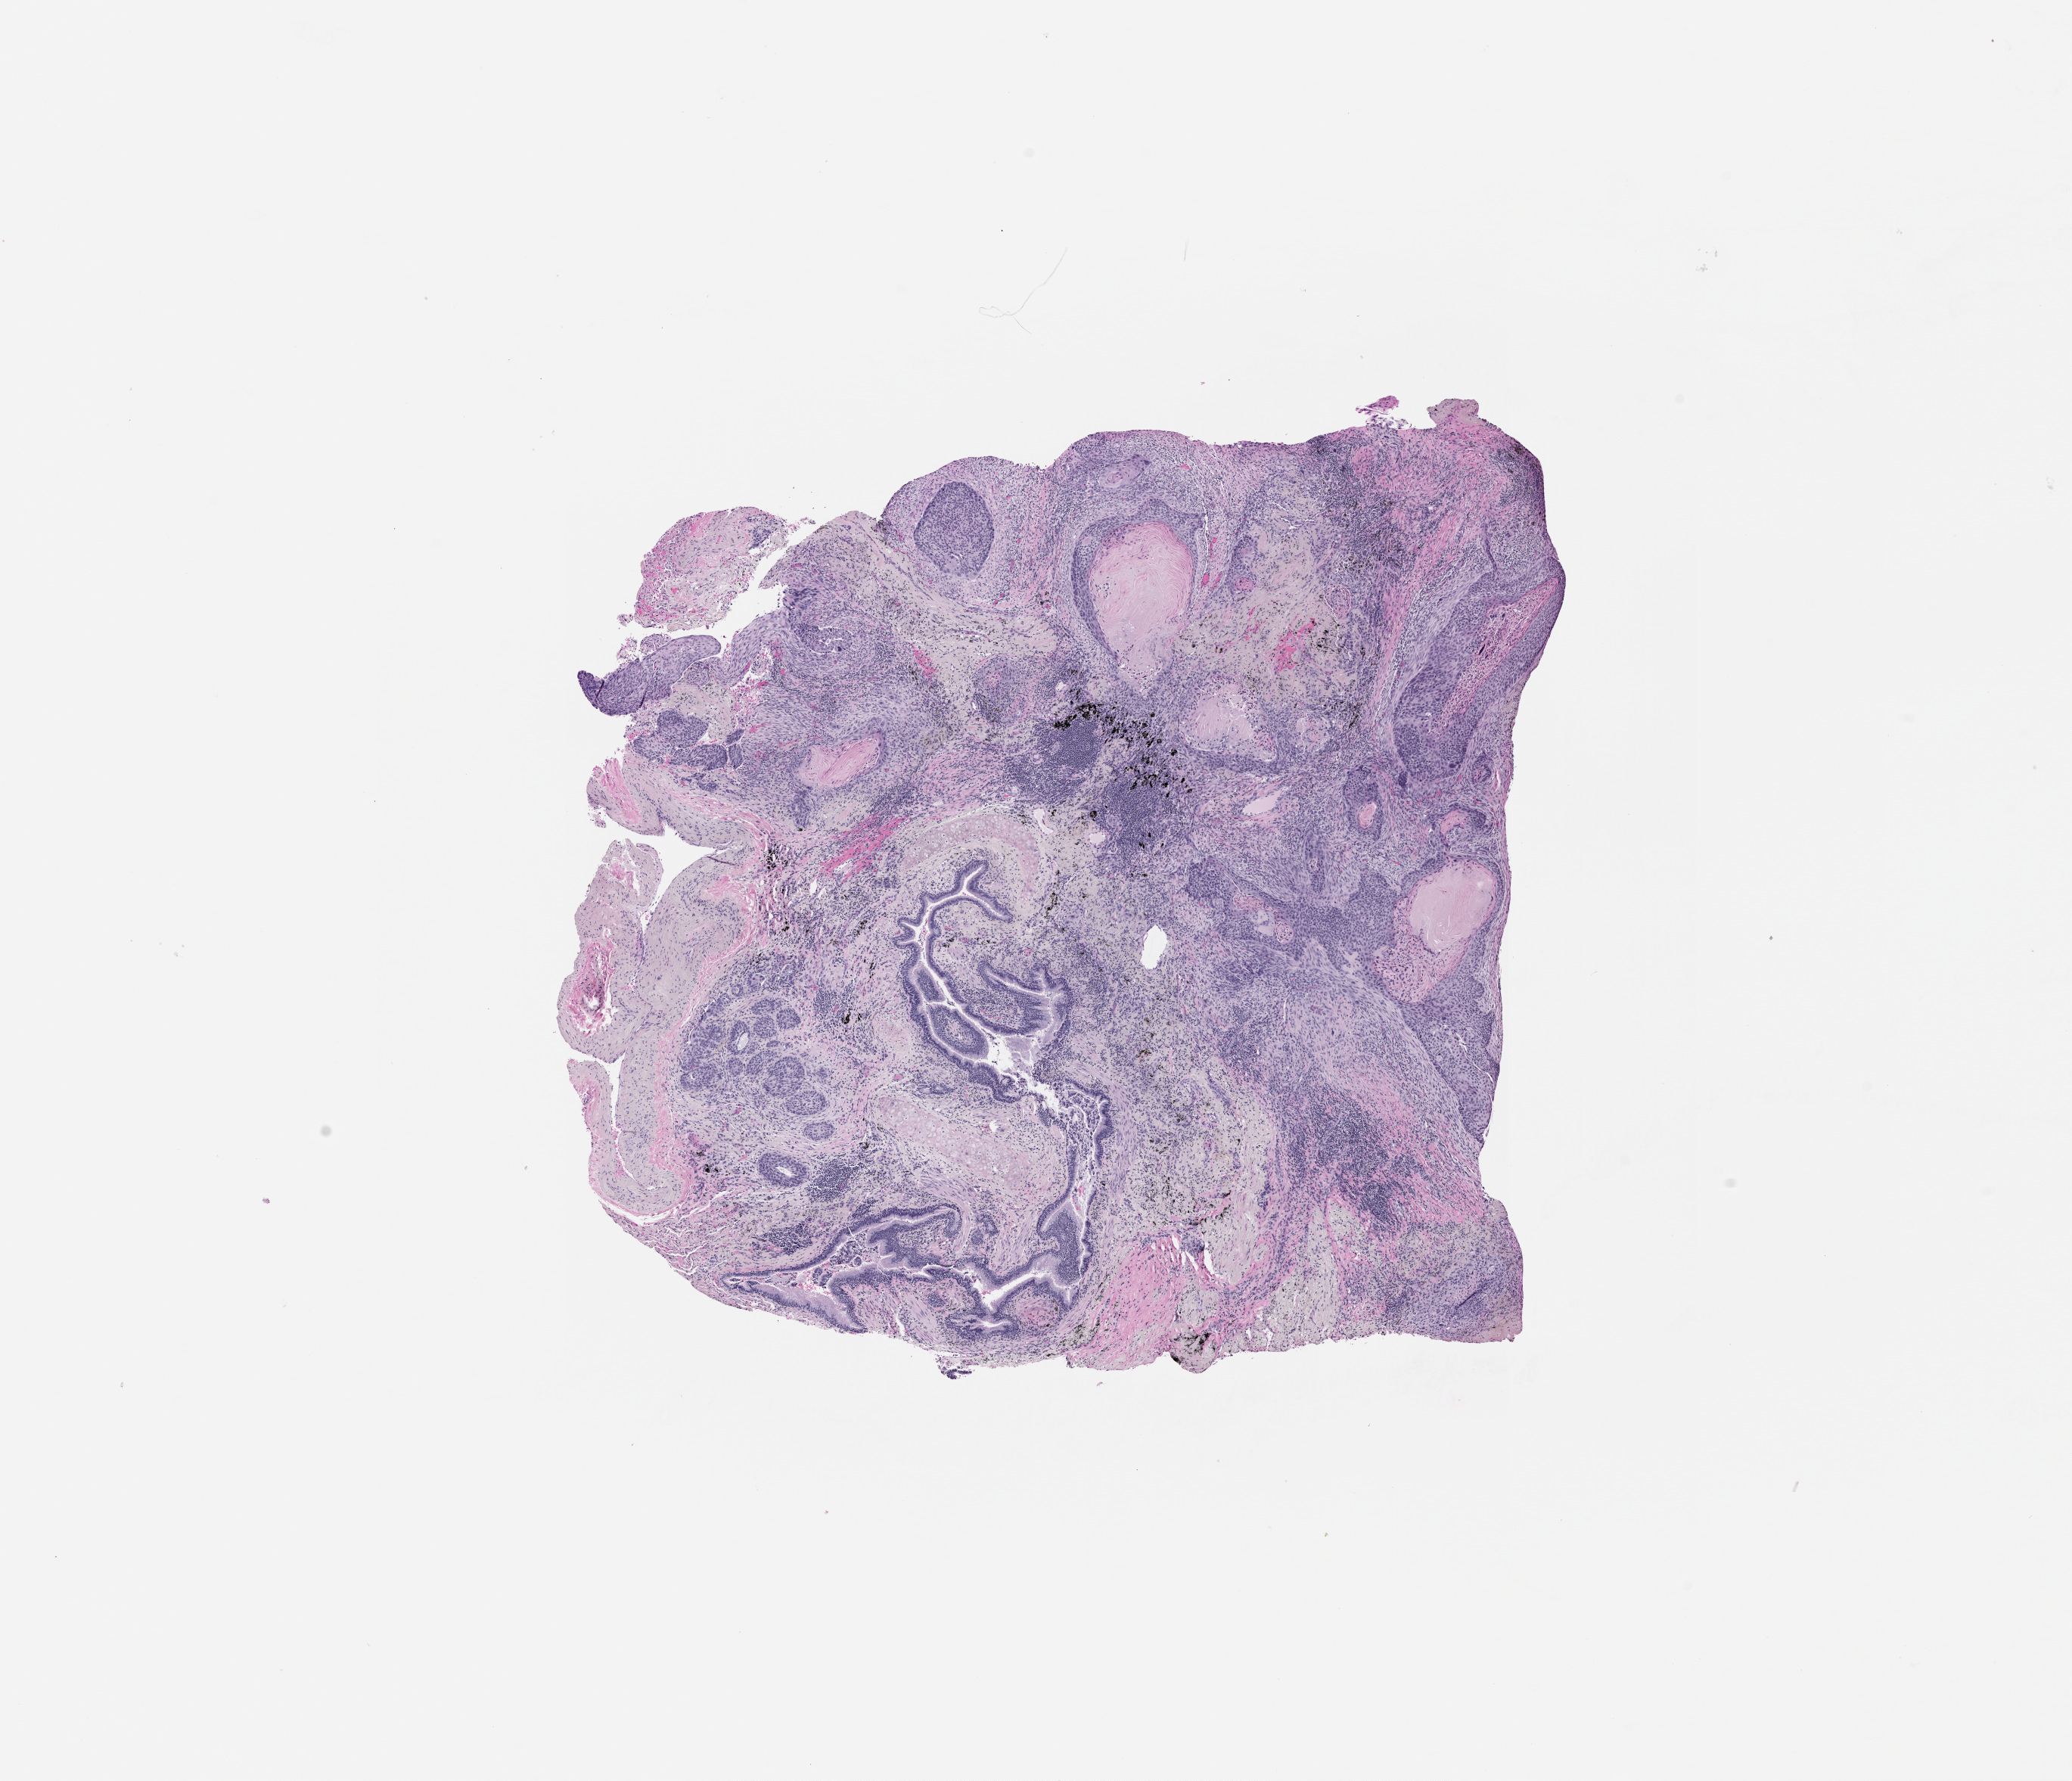
Whole-slide histology image, H&E-stained, shown as a low-resolution overview of the whole scanned area (about 11.0 x 9.5 mm, acquisition: 20x scan). Lung, tumour tissue. Female patient.
Patient diagnosis (cohort enrolment): squamous cell carcinoma (lung).